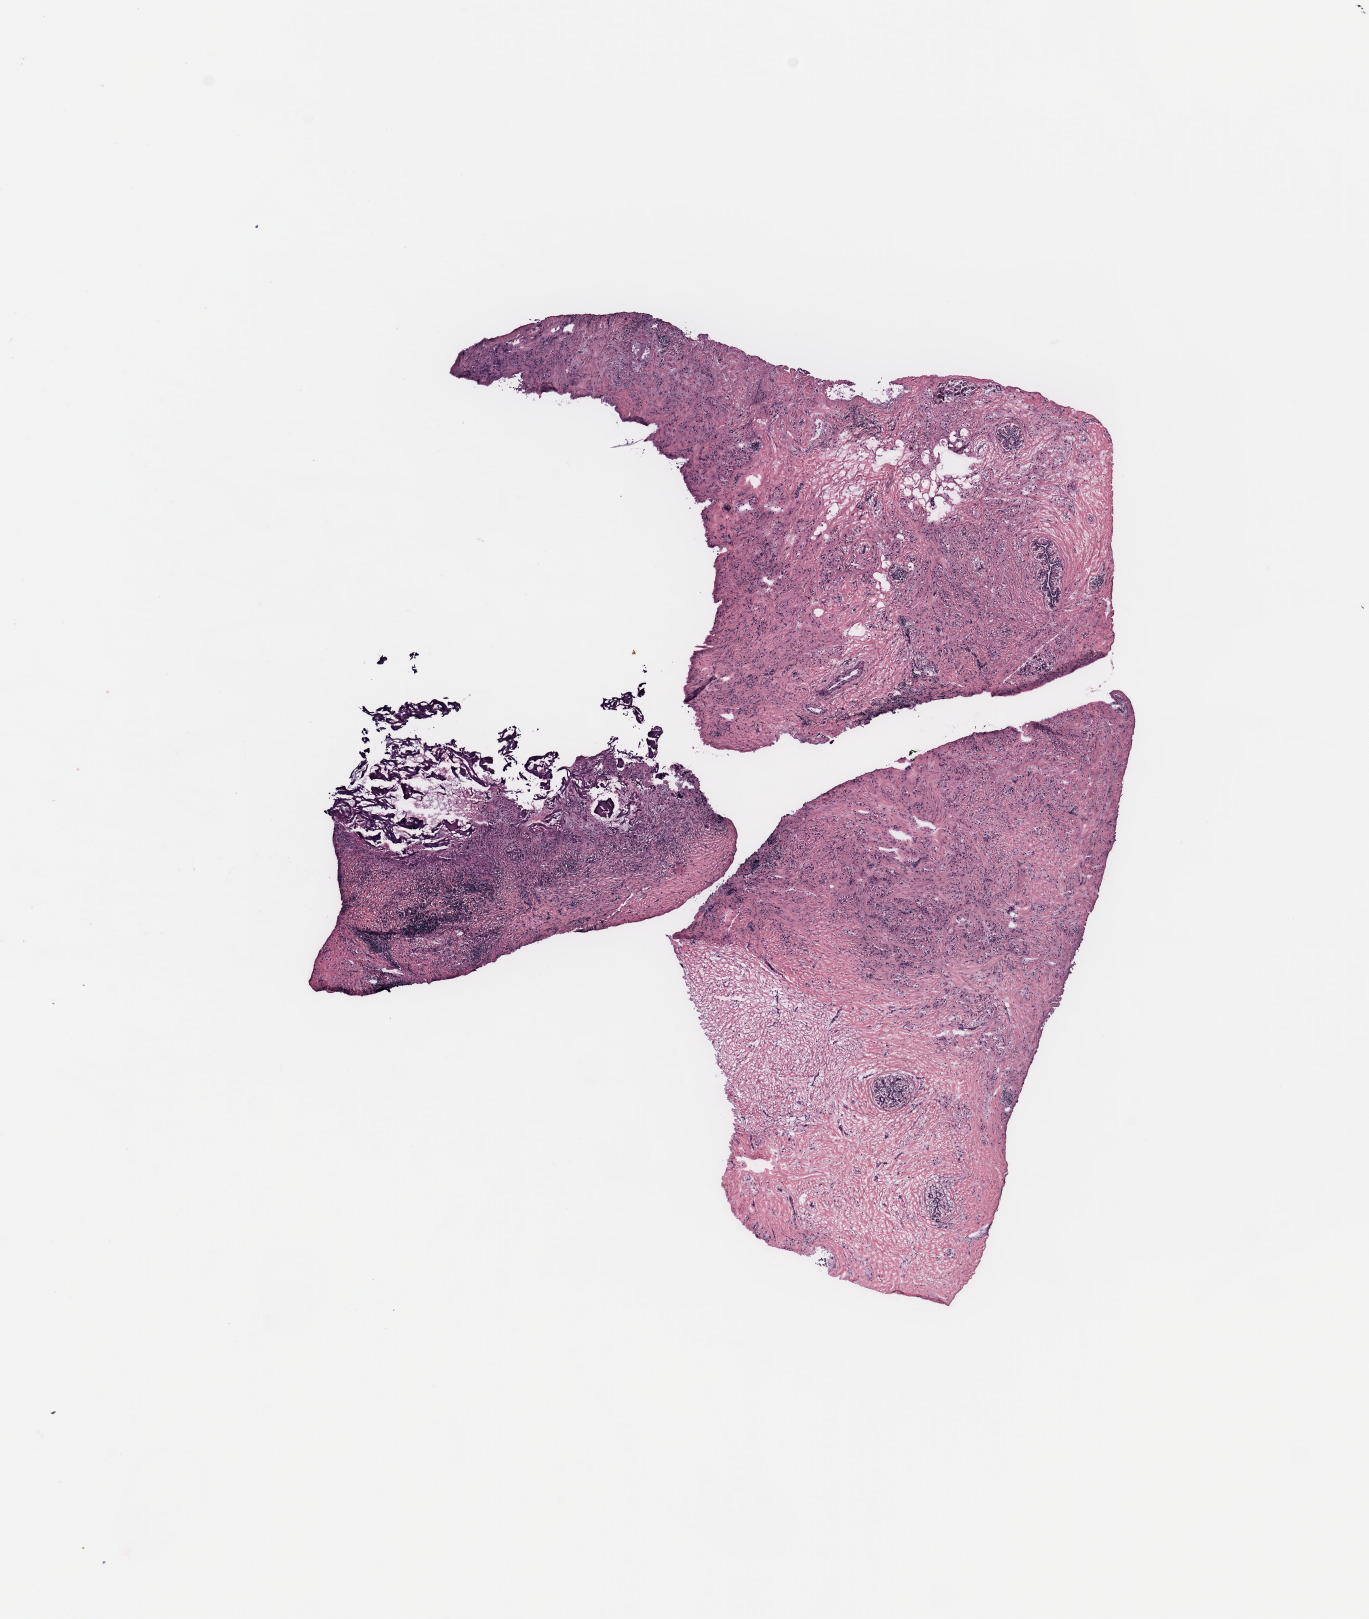
Whole-slide histology image, H&E-stained, low-resolution overview of the scanned area, about 10.8 x 12.8 mm (slide scanned at 20x); breast, tissue type not recorded.
• patient diagnosis (cohort enrolment): breast cancer (breast)